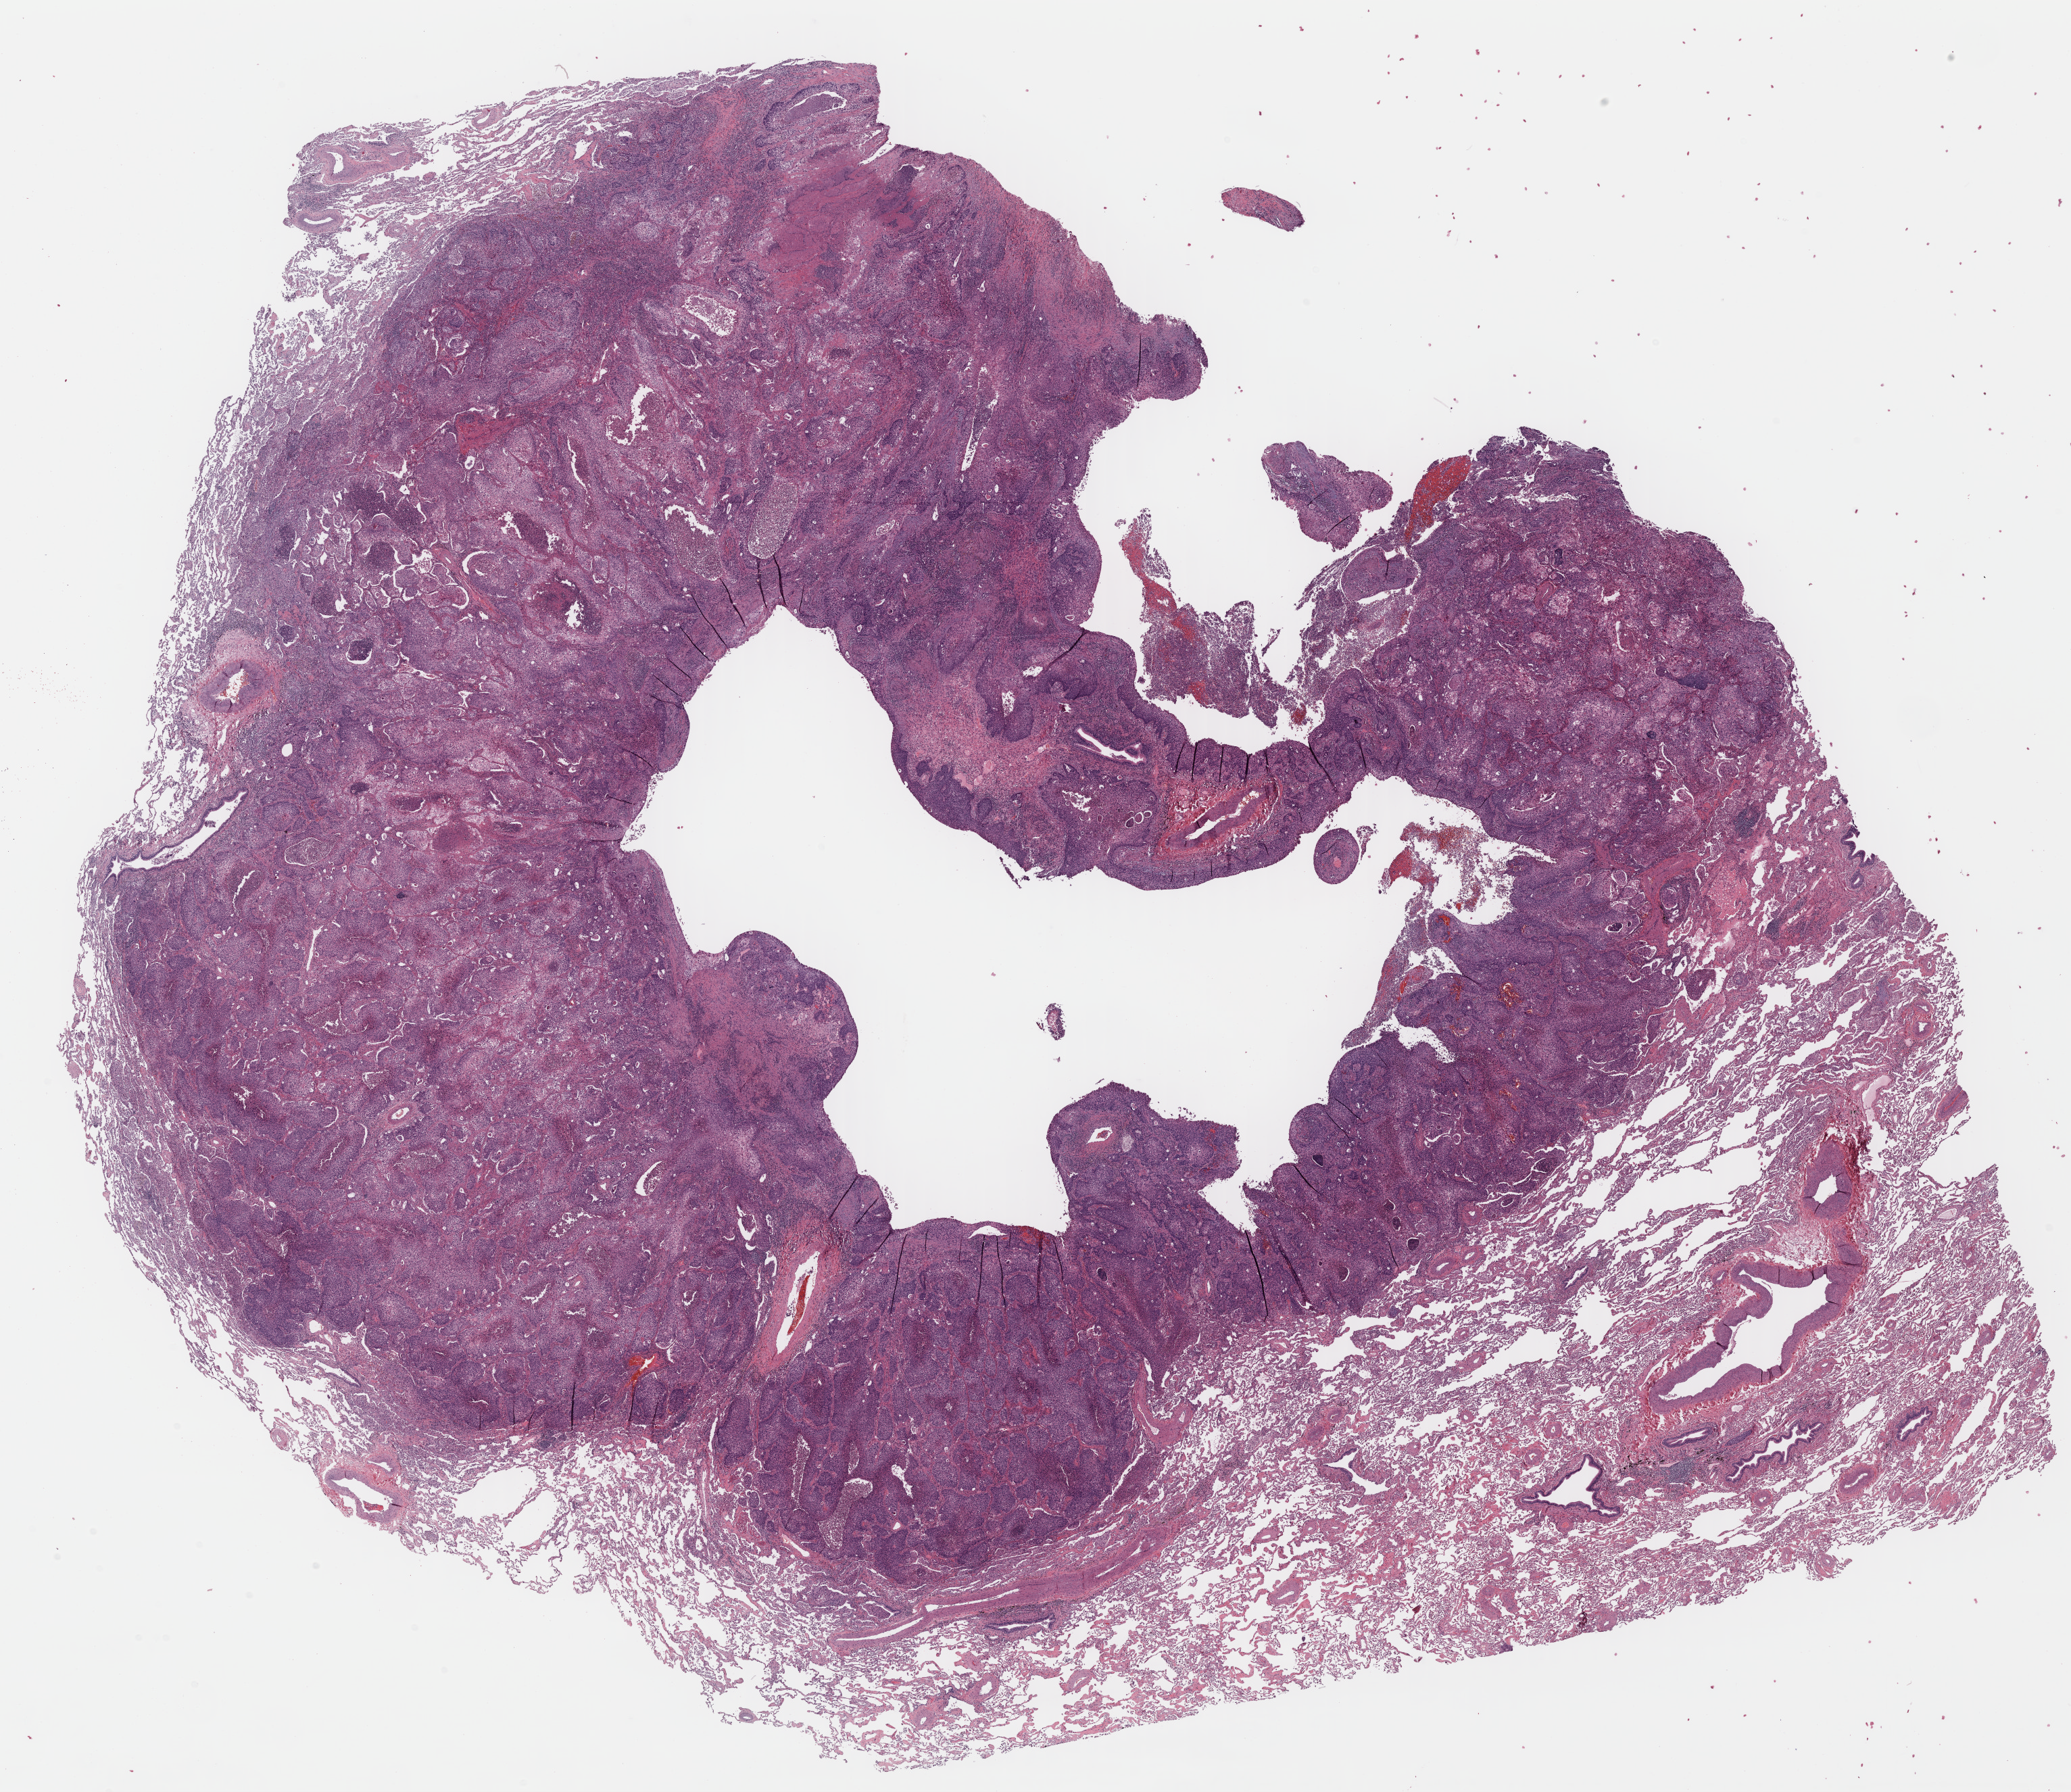
Whole-slide histology image, Hematoxylin and eosin (H&E) stained, whole scanned area (about 24.1 x 20.8 mm) shown as a low-resolution overview, formalin-fixed paraffin-embedded (FFPE) diagnostic section, sample: primary tumour, lung. Patient: male, age at initial diagnosis 71 years.
Diagnosis: Squamous cell carcinoma, NOS (lower lobe, lung). Laterality: right. AJCC pathologic stage: IB (7th edition).